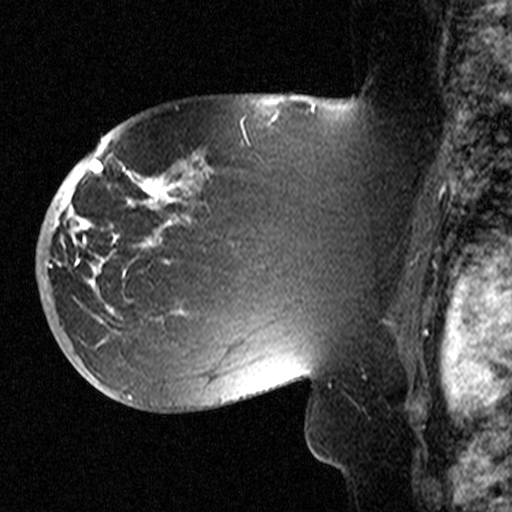
Breast MRI (dynamic contrast-enhanced), one sagittal slice; position 29 of 44 along the scan axis; dynamic contrast-enhanced study with each time point stored as its own series, time point 2 of 3 at this slice position (early post-contrast, ordered by acquisition time); 1.5 T; TE 4.5 ms, TR 11 ms; 3.27 mm slice thickness; 512 × 512 image matrix, field of view 200 × 200 mm. Patient: female, 53 years. Case-level facts recorded for this patient, not image findings: setting: breast cancer imaged before/during neoadjuvant chemotherapy; receptor status: HR-positive, HER2-negative.
Annotated regions visible in this slice (semi-automatic segmentation, software-assisted and operator-edited):
- analysis volume of interest (the breast-tissue region the enhancement analysis was run in; not a lesion): bounding box (x1, y1, x2, y2) in pixels: (58, 154, 311, 367)
- tumour enhancement mask (voxels above the 90 % enhancement threshold inside the analysis volume of interest): (63, 167, 194, 273)